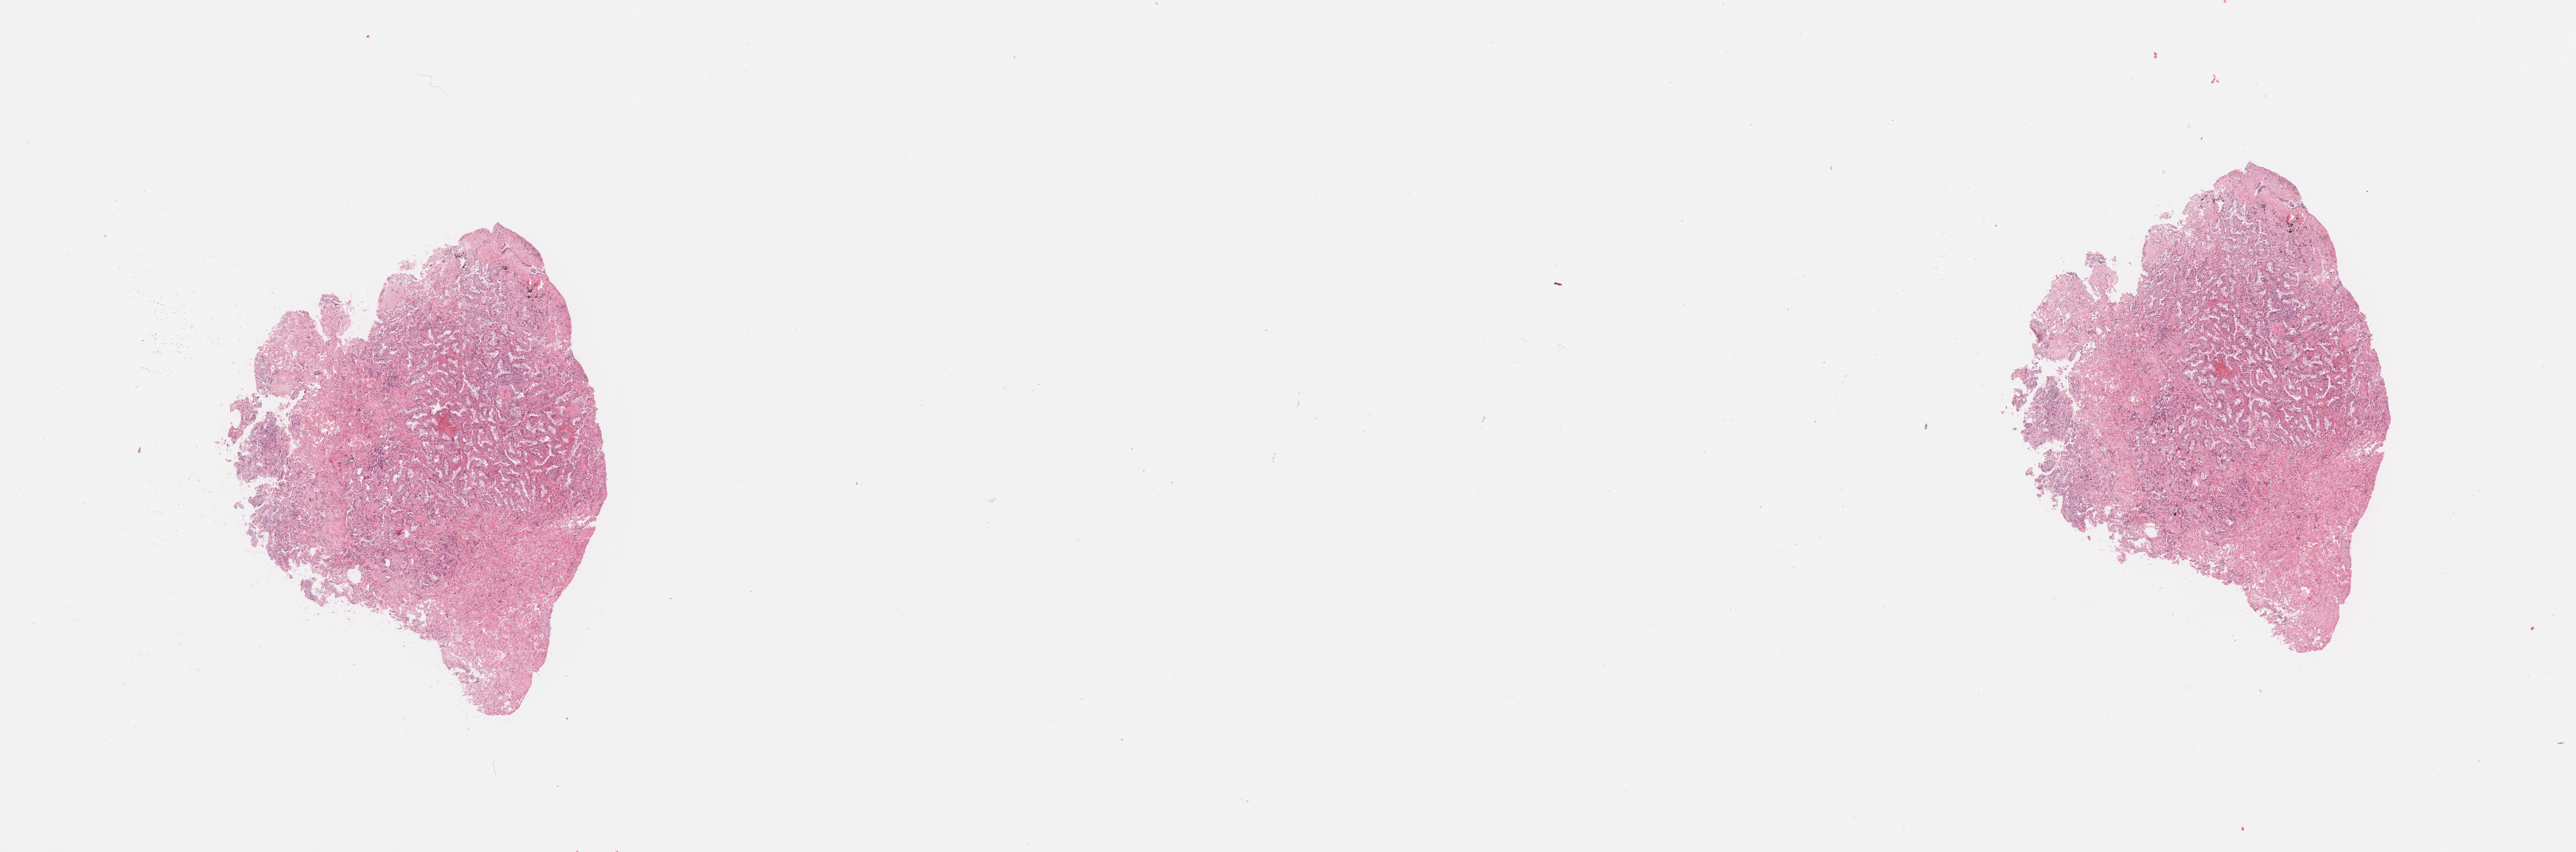
Whole-slide histology image, H&E — low-resolution overview of the scanned area, about 25.6 x 8.5 mm, tumour tissue sample, sampled site: lung. Female, 78 y/o. Histologic grade: G2 (moderately differentiated). Slide review estimates, as recorded: tumour nuclei 75%, necrosis 3%.
AJCC pathologic stage: IIB. Diagnosis: Adenocarcinoma, NOS.